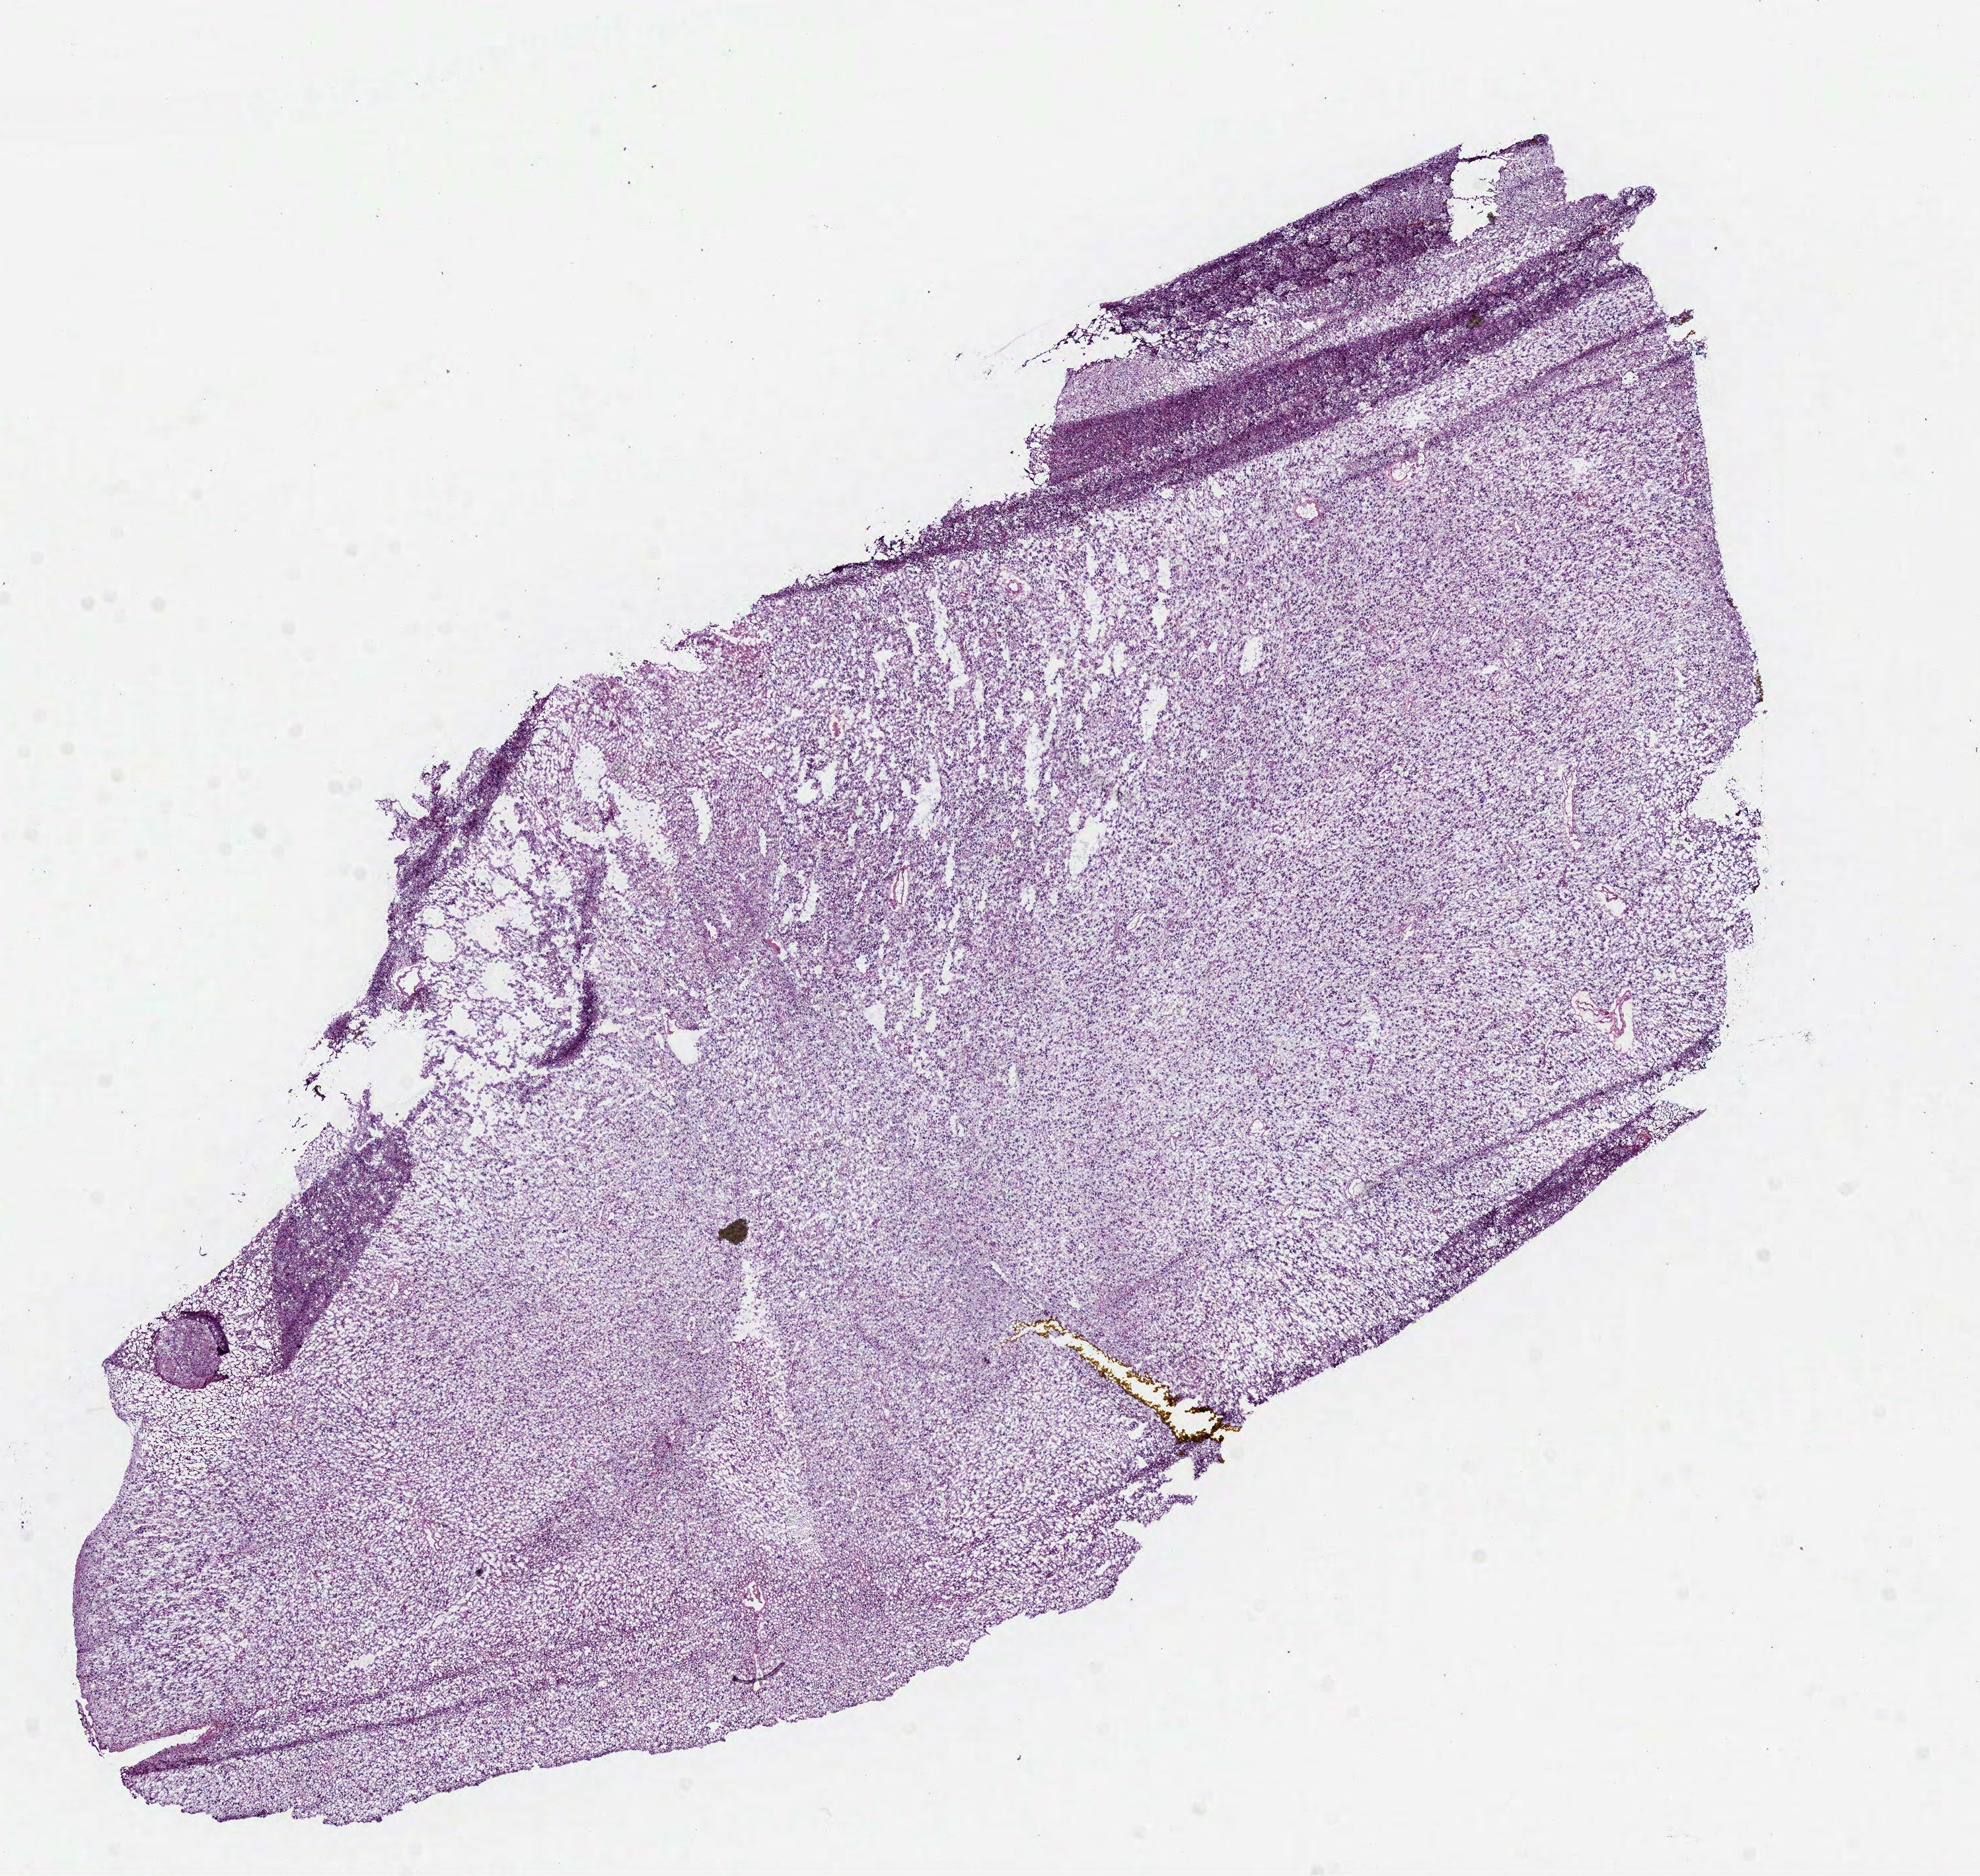
Hematoxylin and eosin (H&E) stained whole-slide image, a low-resolution overview of the entire scanned area, about 12.1 x 11.4 mm; frozen section from the bottom of the tissue portion; brain, primary tumour sample. Male, age 39 years at initial diagnosis. Histologic grade: G3 (poorly differentiated). Pathologist review of this section (percent, as recorded): tumour cells 100%, tumour nuclei 85%, normal cells 0%, stromal cells 0%, necrosis 0%.
- laterality: left
- diagnosis: Astrocytoma, anaplastic (cerebrum)